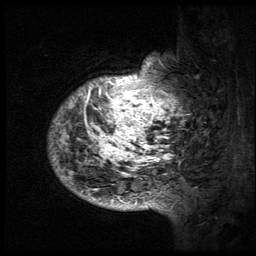
Breast MRI (dynamic contrast-enhanced), one sagittal slice; slice 11 of 64 in the series (ordered by position); 3 images stored at this slice position (order not interpretable as contrast timing); 1.5 T; TE 4.2 ms, TR 9 ms; 256 × 256 image matrix, field of view 180 × 180 mm. Patient: female, 50 years. Case-level facts recorded for this patient, not image findings: setting: breast cancer imaged before/during neoadjuvant chemotherapy; receptor status: triple-negative.
Outlined on this slice (semi-automatic segmentation, software-assisted and operator-edited):
- analysis volume of interest (the breast-tissue region the enhancement analysis was run in; not a lesion): box from (x=48, y=41) to (x=194, y=212) px
- tumour enhancement mask (voxels above the 140 % enhancement threshold inside the analysis volume of interest): (x=49, y=55)–(x=186, y=212)